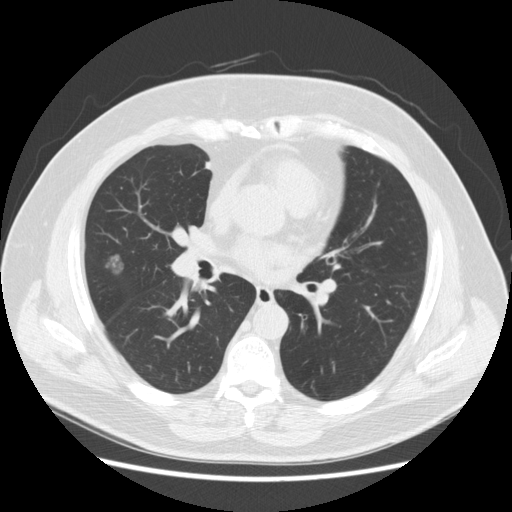
Low-dose screening chest CT, axial slice, baseline screening round, lung window (W 1500 / L -600 HU). Male, age 67 years at enrolment.
- Lesion marked by an expert reader, bounding box <94,251,129,283> (left, top, right, bottom; pixels).
- Screening reader's record for this exam (one nodule recorded; not confirmed to be the boxed lesion): non-calcified nodule or mass ≥4 mm, right middle lobe, 15 × 11 mm, smooth margins, soft tissue attenuation.
- Official screen result: positive, change unspecified: nodule(s) >= 4 mm or enlarging nodule(s), mass(es), or other non-specific abnormalities suspicious for lung cancer.
- Participant outcome: lung cancer diagnosed 409 days after this screen — adenocarcinoma, NOS, right middle lobe, moderately differentiated (G2), stage IA (AJCC 6th edition), 14 mm at pathology.